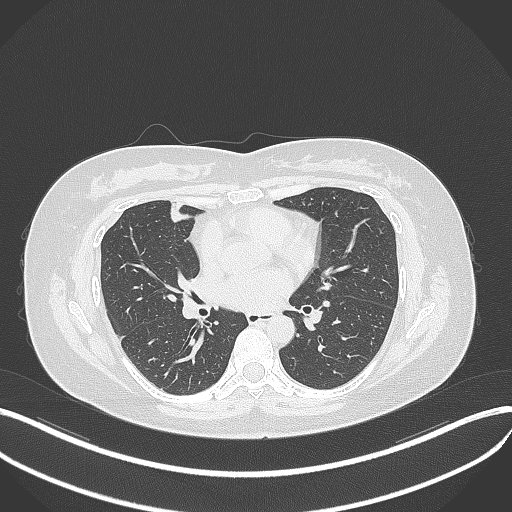
Chest CT, one axial slice. Position 157 of 273 along the scan axis. Lung window (W 1500 / L -600 HU). 1 mm slice thickness. 512 × 512 image matrix, field of view 400 × 400 mm. Female patient, age 42 years. From the clinical record (not read from this slice): clinical TNM (as recorded): T1b N0 M0.
Annotated regions visible in this slice (rectangle marked by the reading radiologist):
- lung tumour (recorded histology: adenocarcinoma): box from (x=167, y=201) to (x=191, y=227) px